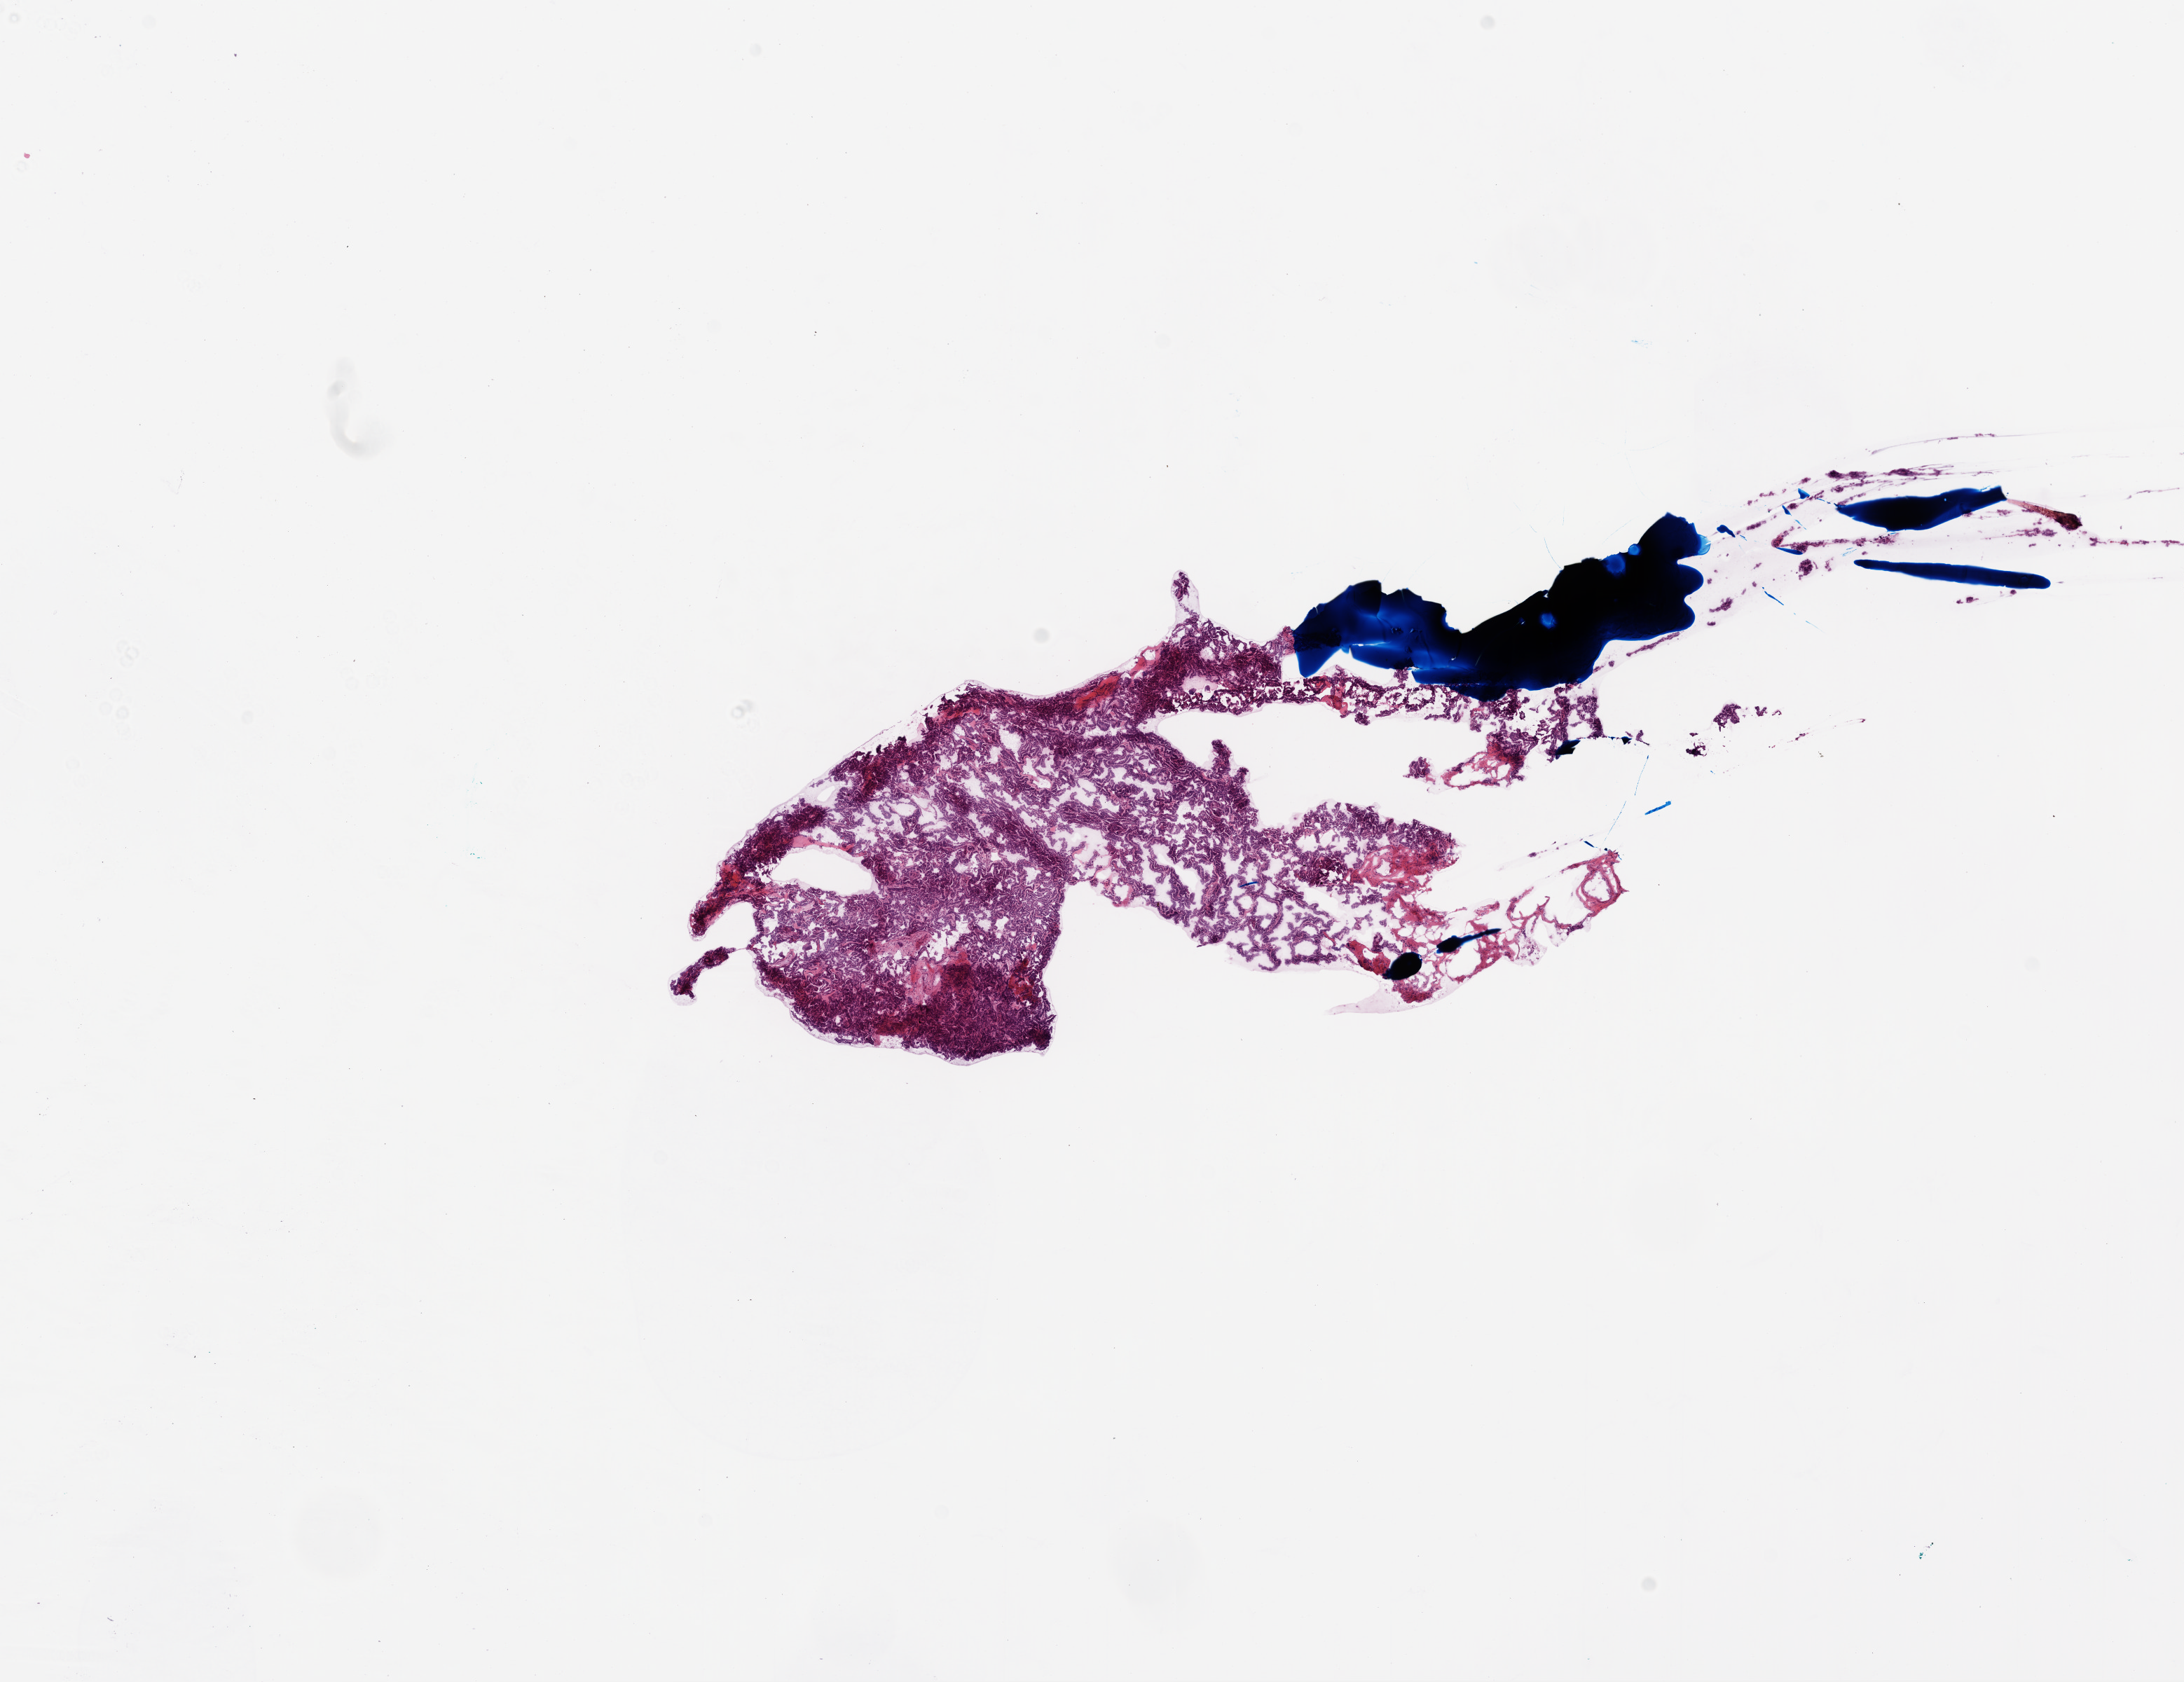
Digitized H&E-stained tissue section (whole slide), shown as a low-resolution overview of the whole scanned area (about 12.6 x 9.7 mm, from a 20x scan); frozen section from the top of the tissue portion; ovary, primary tumour sample. Patient: female, age at initial diagnosis 63 years. Histologic grade: G3 (poorly differentiated). Slide review estimates, as recorded: tumour cells 95%, tumour nuclei 99%, normal cells 5%, stromal cells 0%, necrosis 0%.
- histologic diagnosis: Serous cystadenocarcinoma, NOS
- laterality: bilateral
- FIGO stage: IIIC